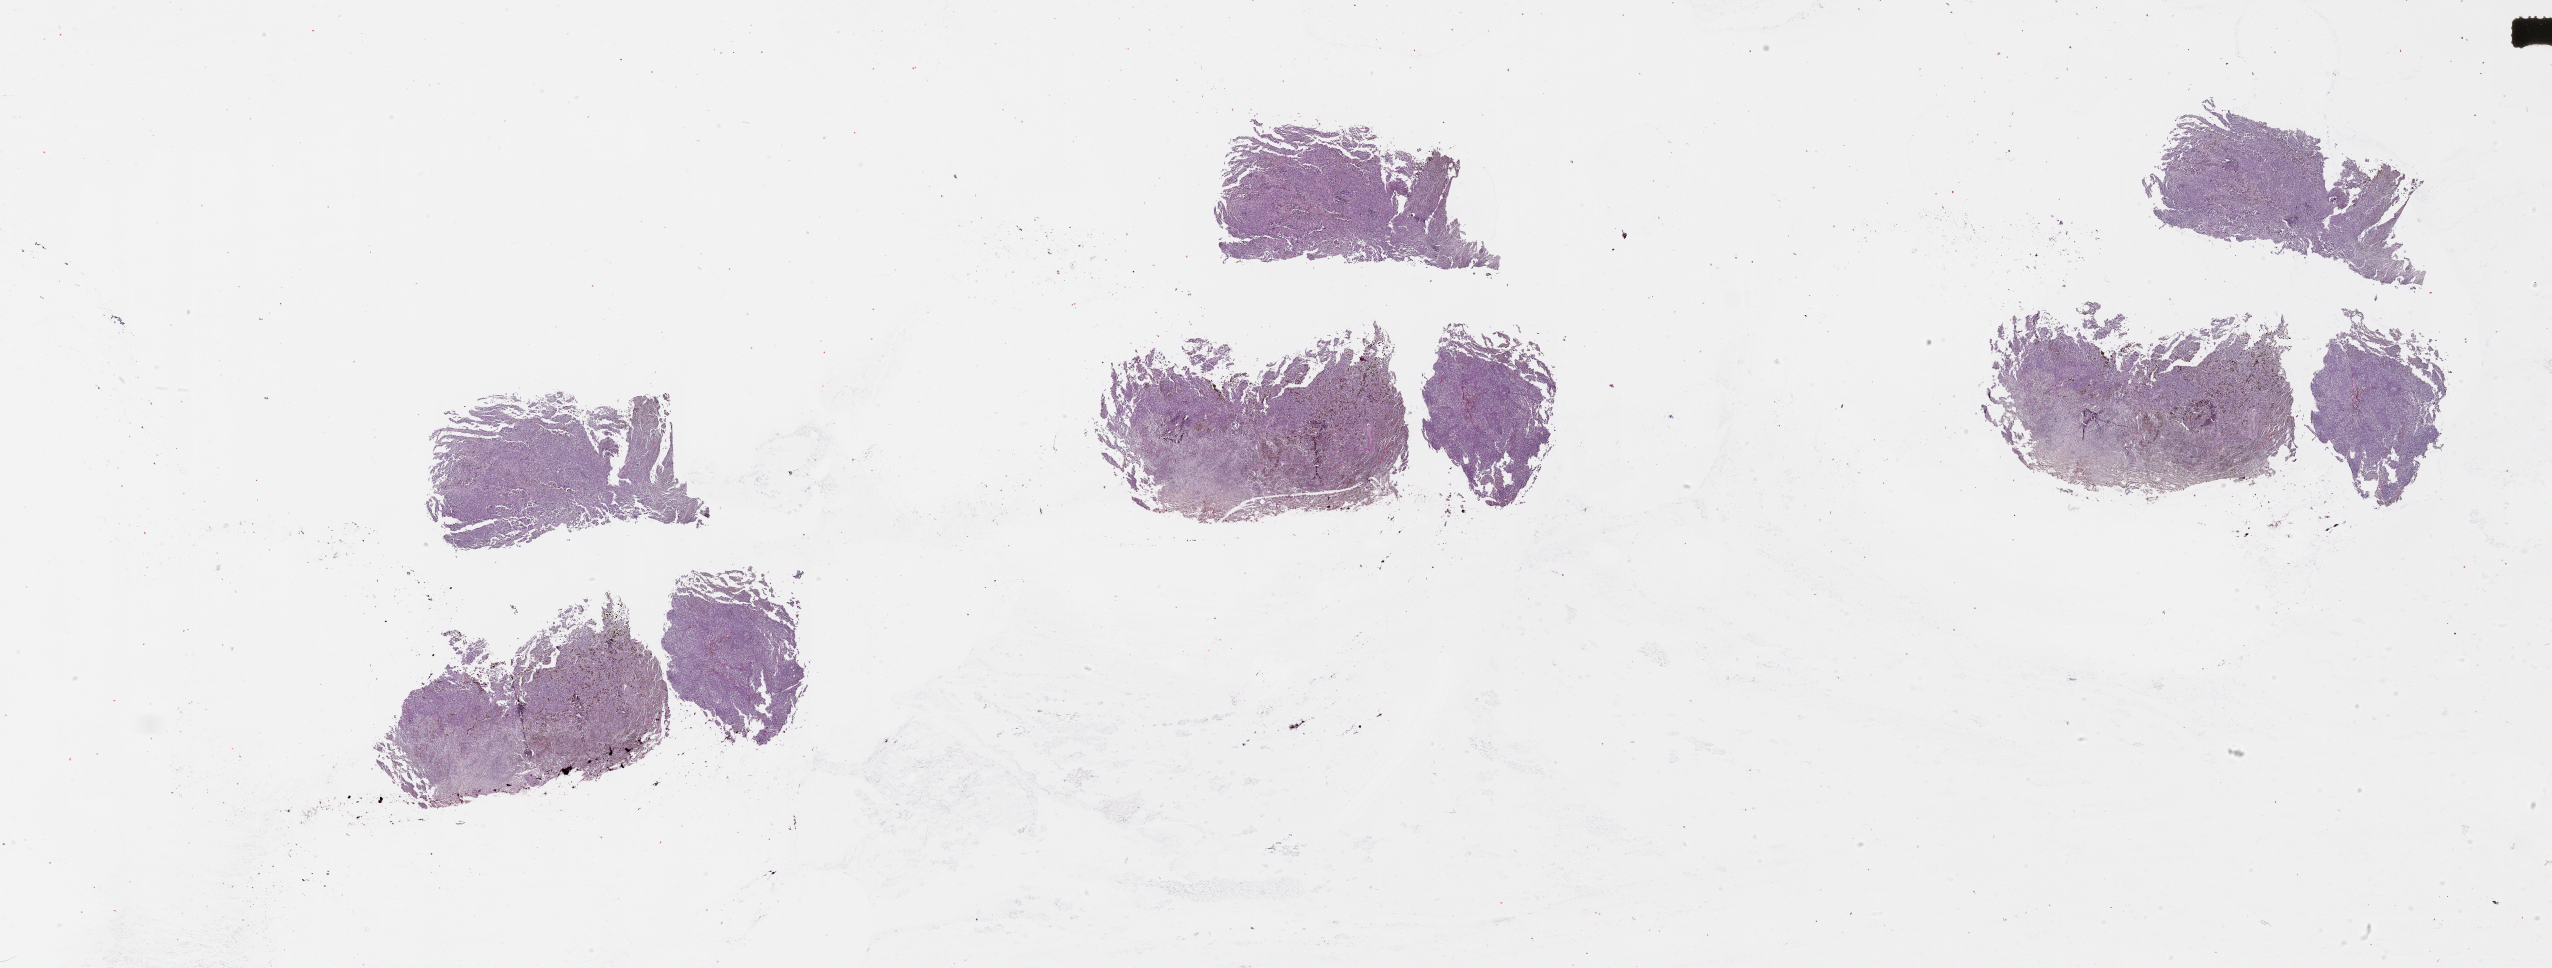
Whole-slide histology image, Hematoxylin and eosin (H&E) stained, a low-resolution overview of the entire scanned area, about 41.1 x 15.6 mm (from a 20x scan); tumour tissue sample, sampled site: skin. Female, 70 y/o. Slide review estimates, as recorded: tumour nuclei 80%, necrosis 0%.
AJCC pathologic stage: IIIC. Histologic diagnosis: Malignant melanoma, NOS.